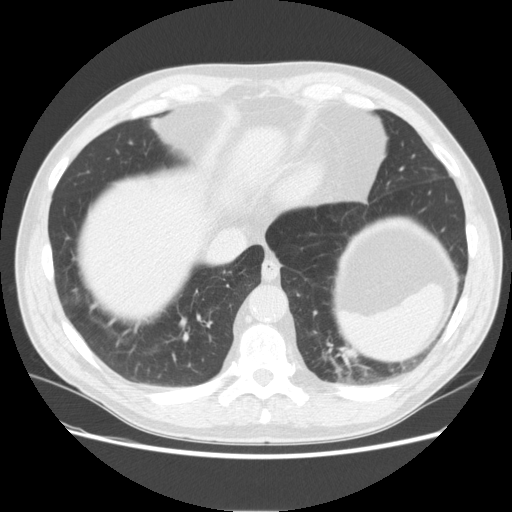
Low-dose screening chest CT, one axial slice; reconstruction kernel STANDARD; 120 kVp; lung window (W 1500 / L -600 HU); 2.5 mm slice thickness; 512 × 512 image matrix, field of view 375 × 375 mm.
Annotated regions visible in this slice (expert manual segmentation):
- lesion 1 (tumor, upper lobe of left lung): box from (x=327, y=347) to (x=364, y=382) px